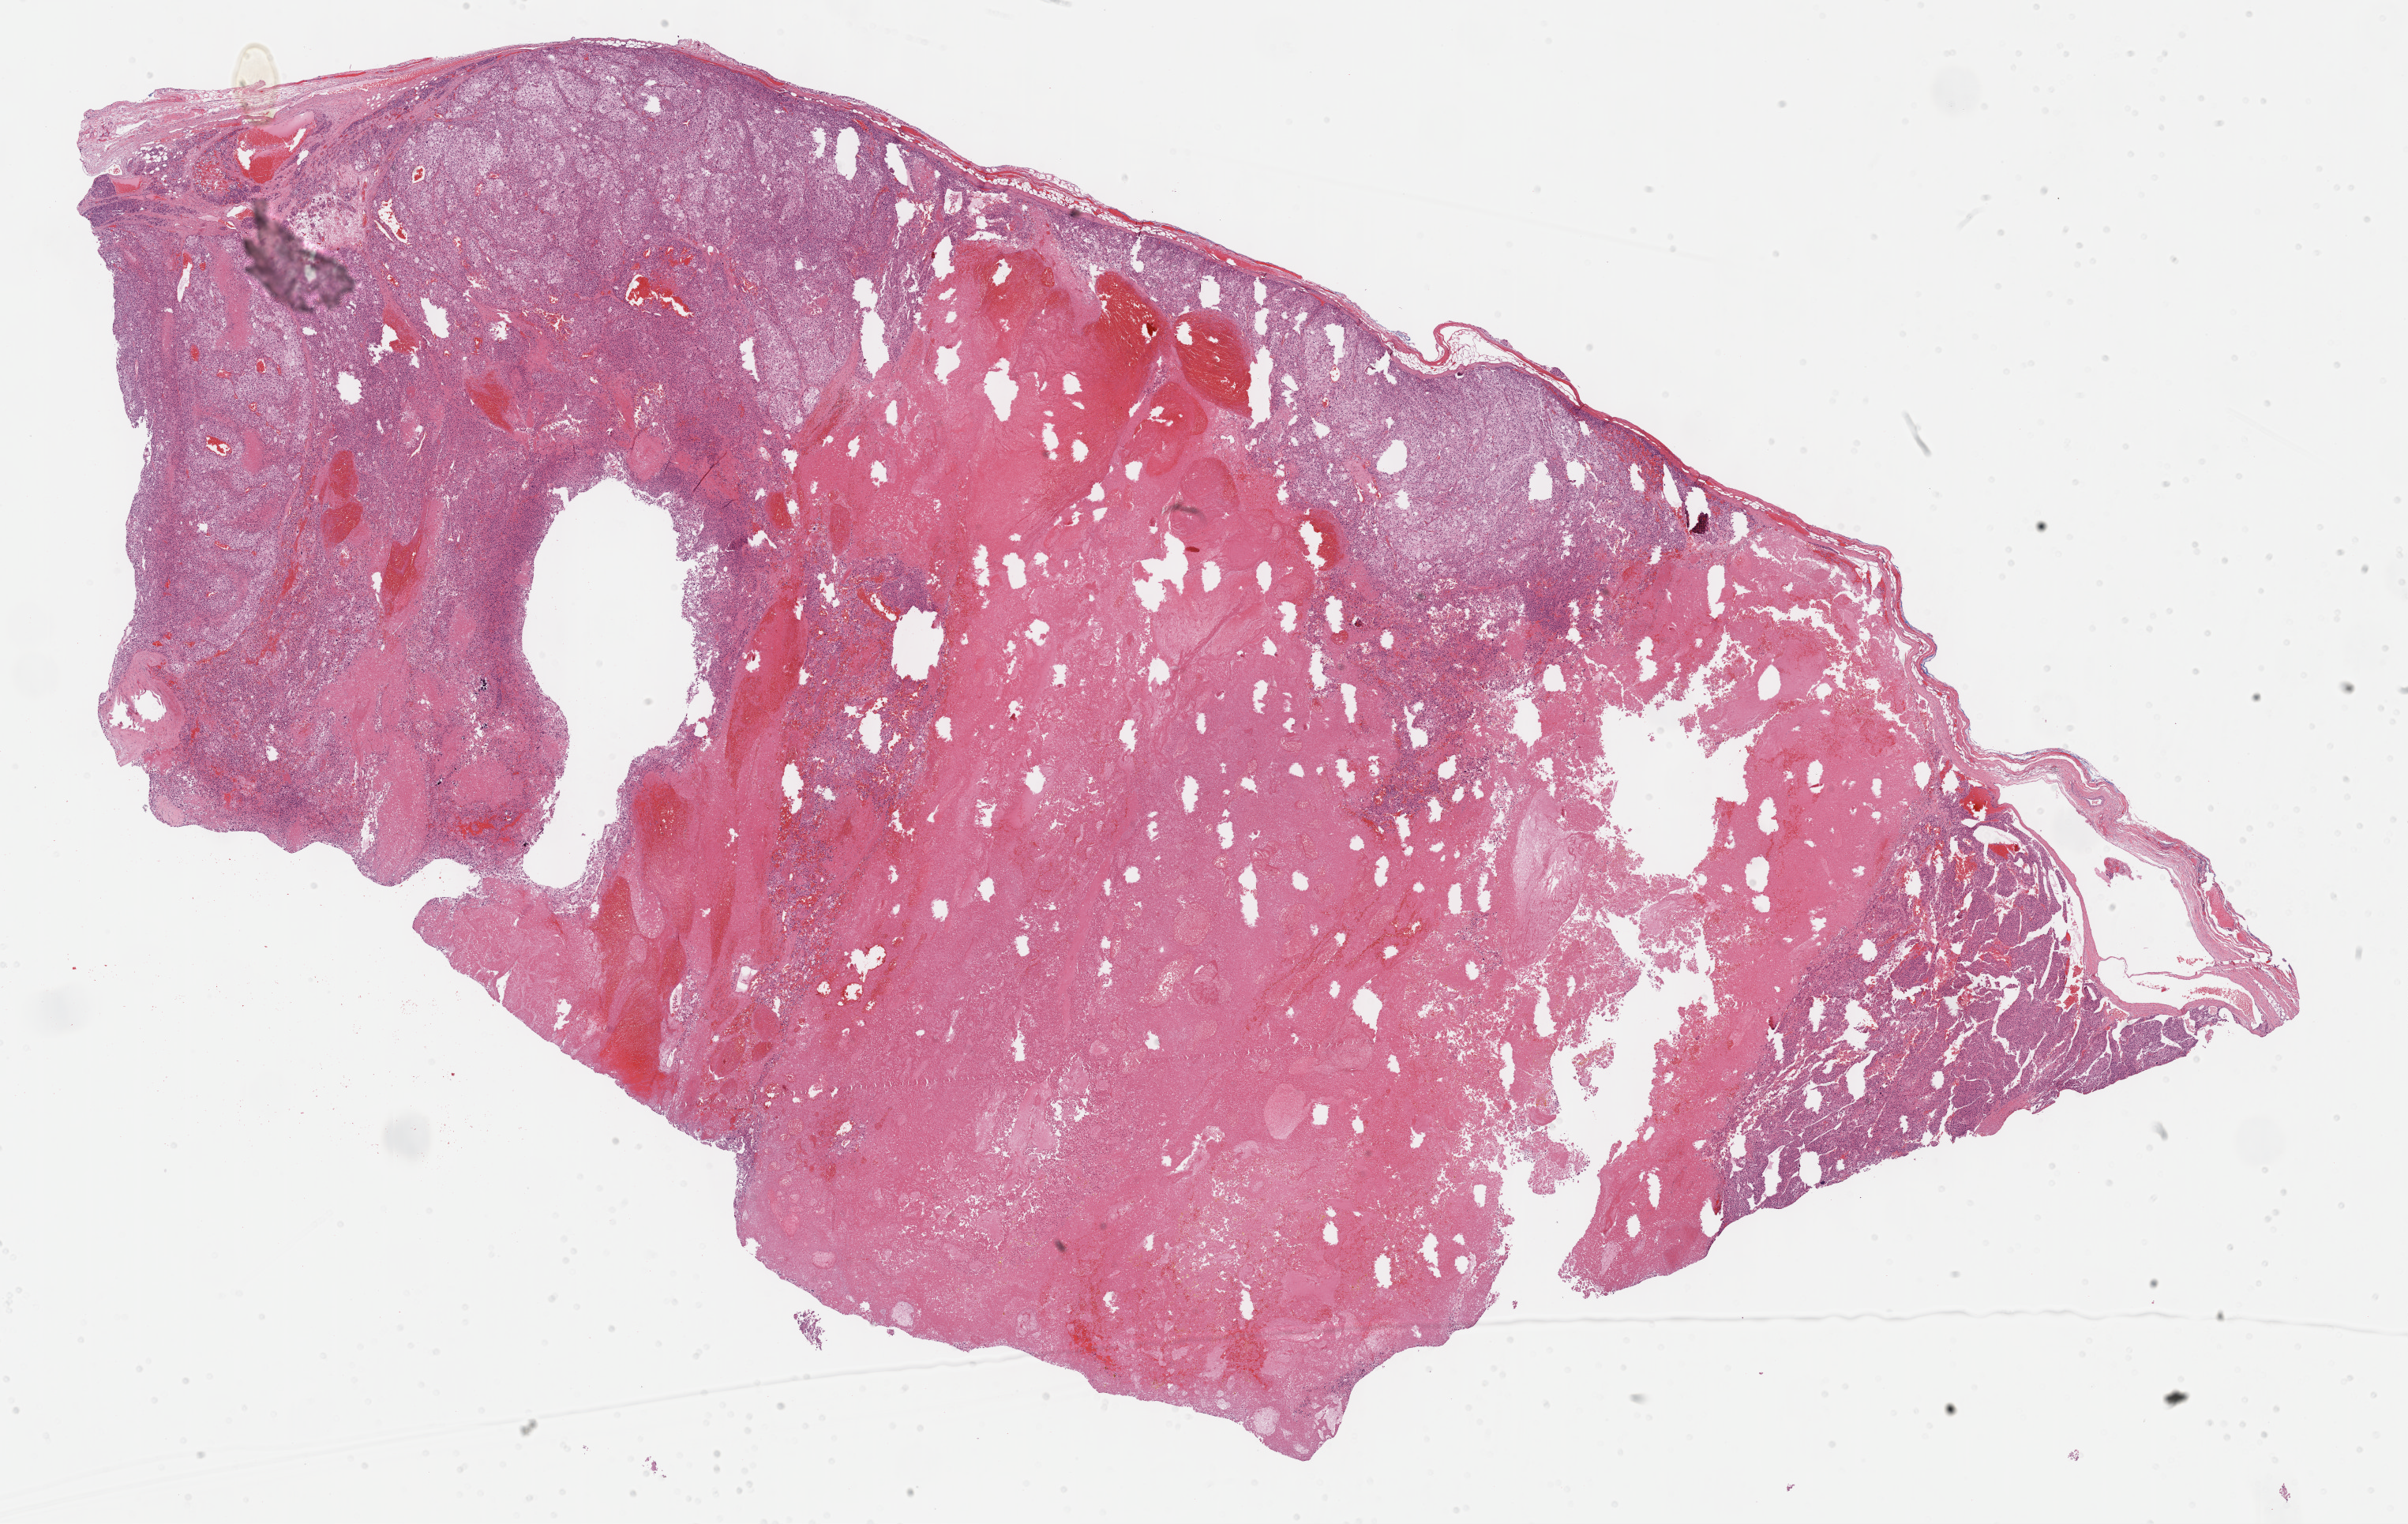
Digitized H&E tissue section (whole slide), whole scanned area (about 24.7 x 15.6 mm) shown as a low-resolution overview, formalin-fixed paraffin-embedded (FFPE) diagnostic section, sample: primary tumour, adrenal cortex. Patient: female, age at initial diagnosis 68 years.
Laterality: right. Pathologic diagnosis: Adrenal cortical carcinoma (cortex of adrenal gland).